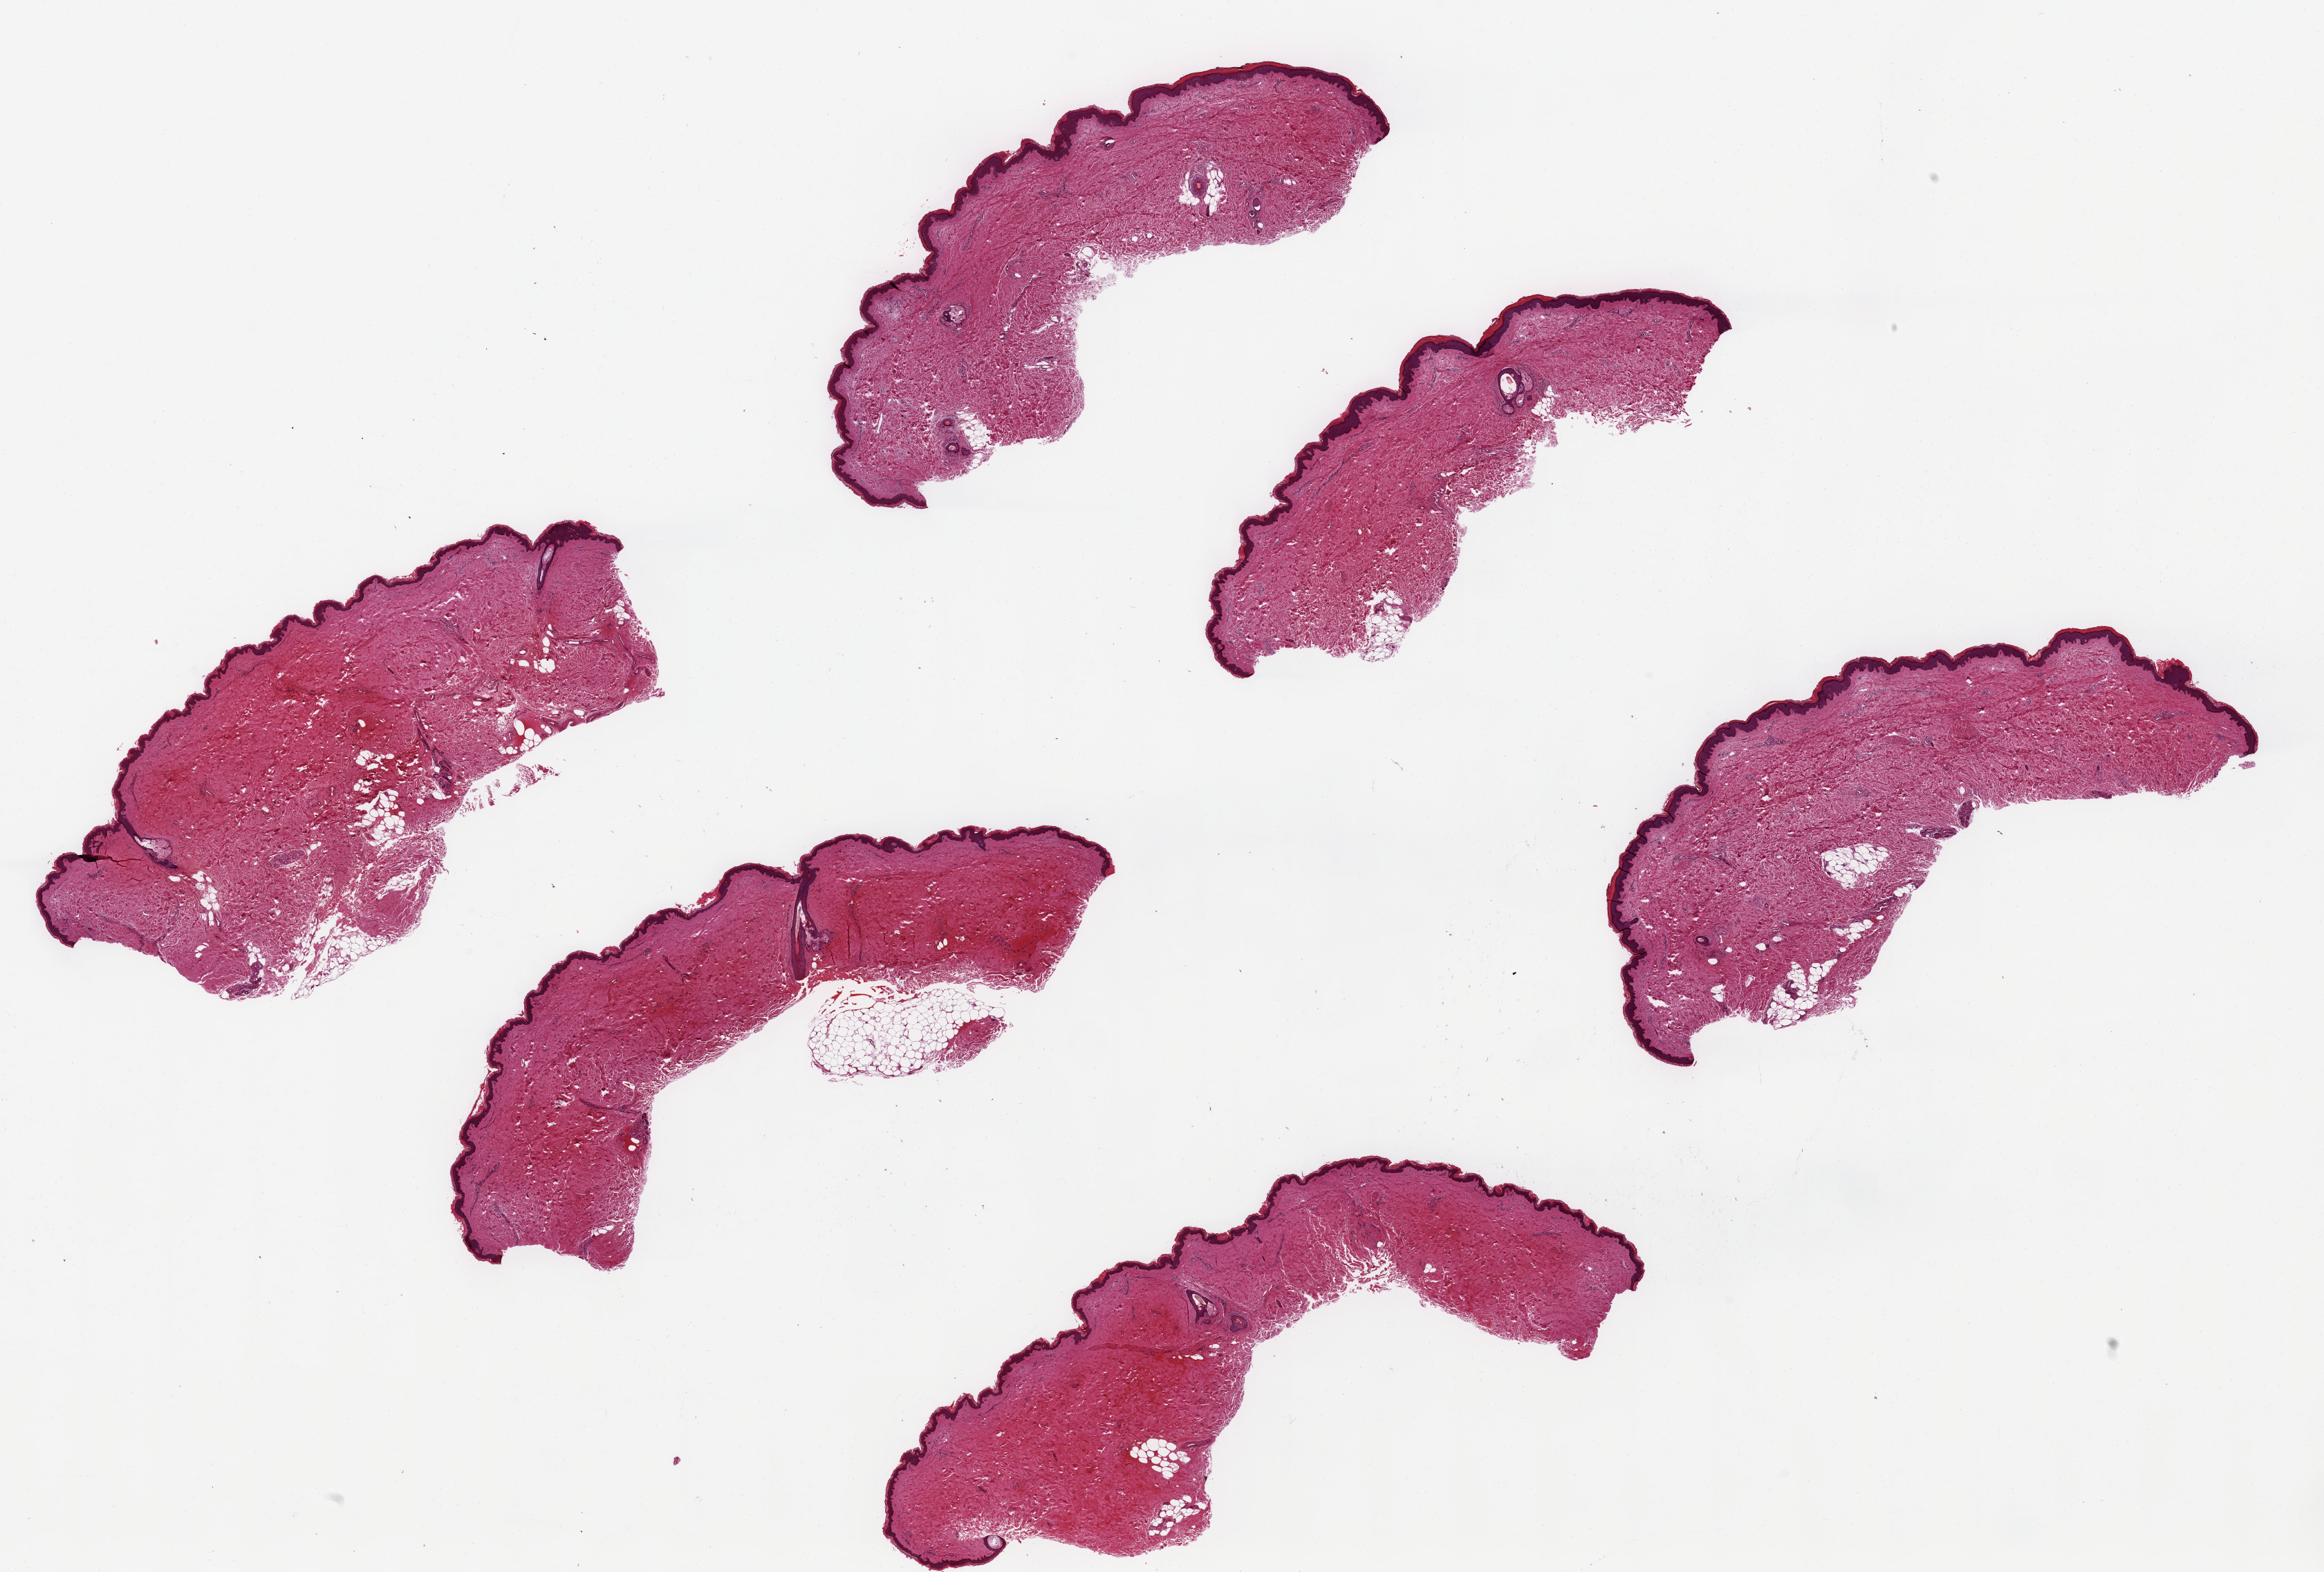
Hematoxylin and eosin (H&E) whole-slide image, low-resolution overview of the scanned area, about 26.6 x 18.0 mm; PAXgene-fixed paraffin-embedded (PFPE) section; target tissue: skin of lower leg; tissue donor sample. Donor: female.
Review note (as recorded): 6 pieces, ~8x3mm. focal dermal hemorrhages.